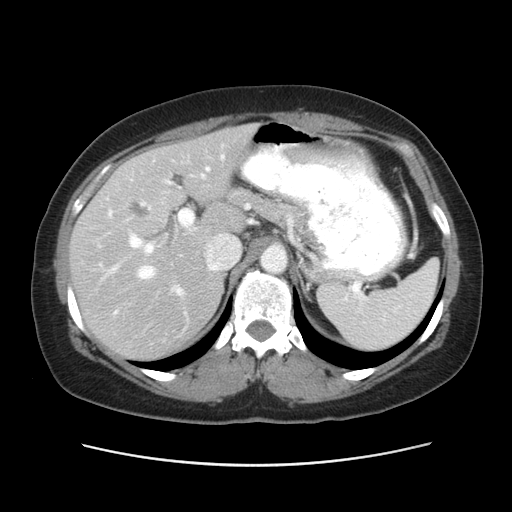
Contrast-enhanced abdominal CT, one axial slice; position 35 of 52 along the scan axis; reconstruction kernel STANDARD; intravenous contrast given; soft-tissue window (W 400 / L 40 HU); 5 mm slice thickness; 512 × 512 image matrix, field of view 362 × 362 mm. Female patient, age 48 years. Case-level facts recorded for this patient, not image findings: diagnosis: colorectal cancer liver metastases, imaged before liver resection; multiple liver metastases: yes; largest metastasis: 4.5 cm; disease in both lobes: yes.
Structures marked on this image (manually delineated by an expert):
- hepatic veins: bounding box (x1, y1, x2, y2) in pixels: (103, 155, 225, 280)
- liver: (70, 127, 253, 360)
- planned liver remnant (the part of the liver to remain after resection): (147, 126, 253, 235)
- portal vein (with intrahepatic branches): (97, 167, 210, 330)
- liver metastasis: (129, 202, 151, 222)